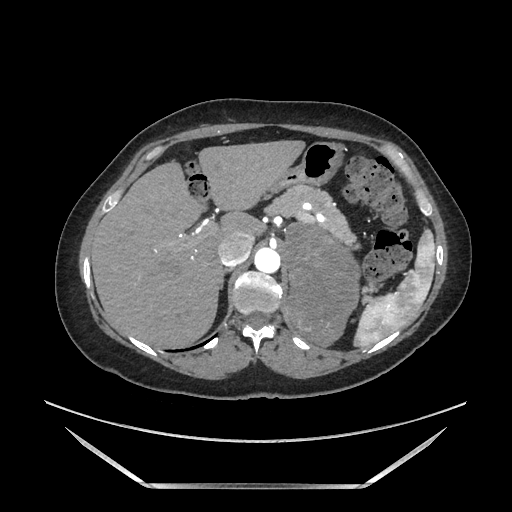
Contrast-enhanced abdominal CT, one axial slice. Slice 126 of 205 in the series (ordered by position). Soft-tissue window (W 400 / L 40 HU). 1.25 mm slice thickness. 512 × 512 image matrix, field of view 440 × 440 mm. Female patient. Case-level facts recorded for this patient, not image findings: diagnosis: adrenocortical carcinoma; tumour side: left adrenal; tumour size at pathology: 12.5 cm; Ki-67 index: 39 %; stage (as recorded): 3.
Structures marked on this image (semi-automatic segmentation, software-assisted and operator-edited):
- mass: bounding box <287,224,361,344> (left, top, right, bottom; pixels)